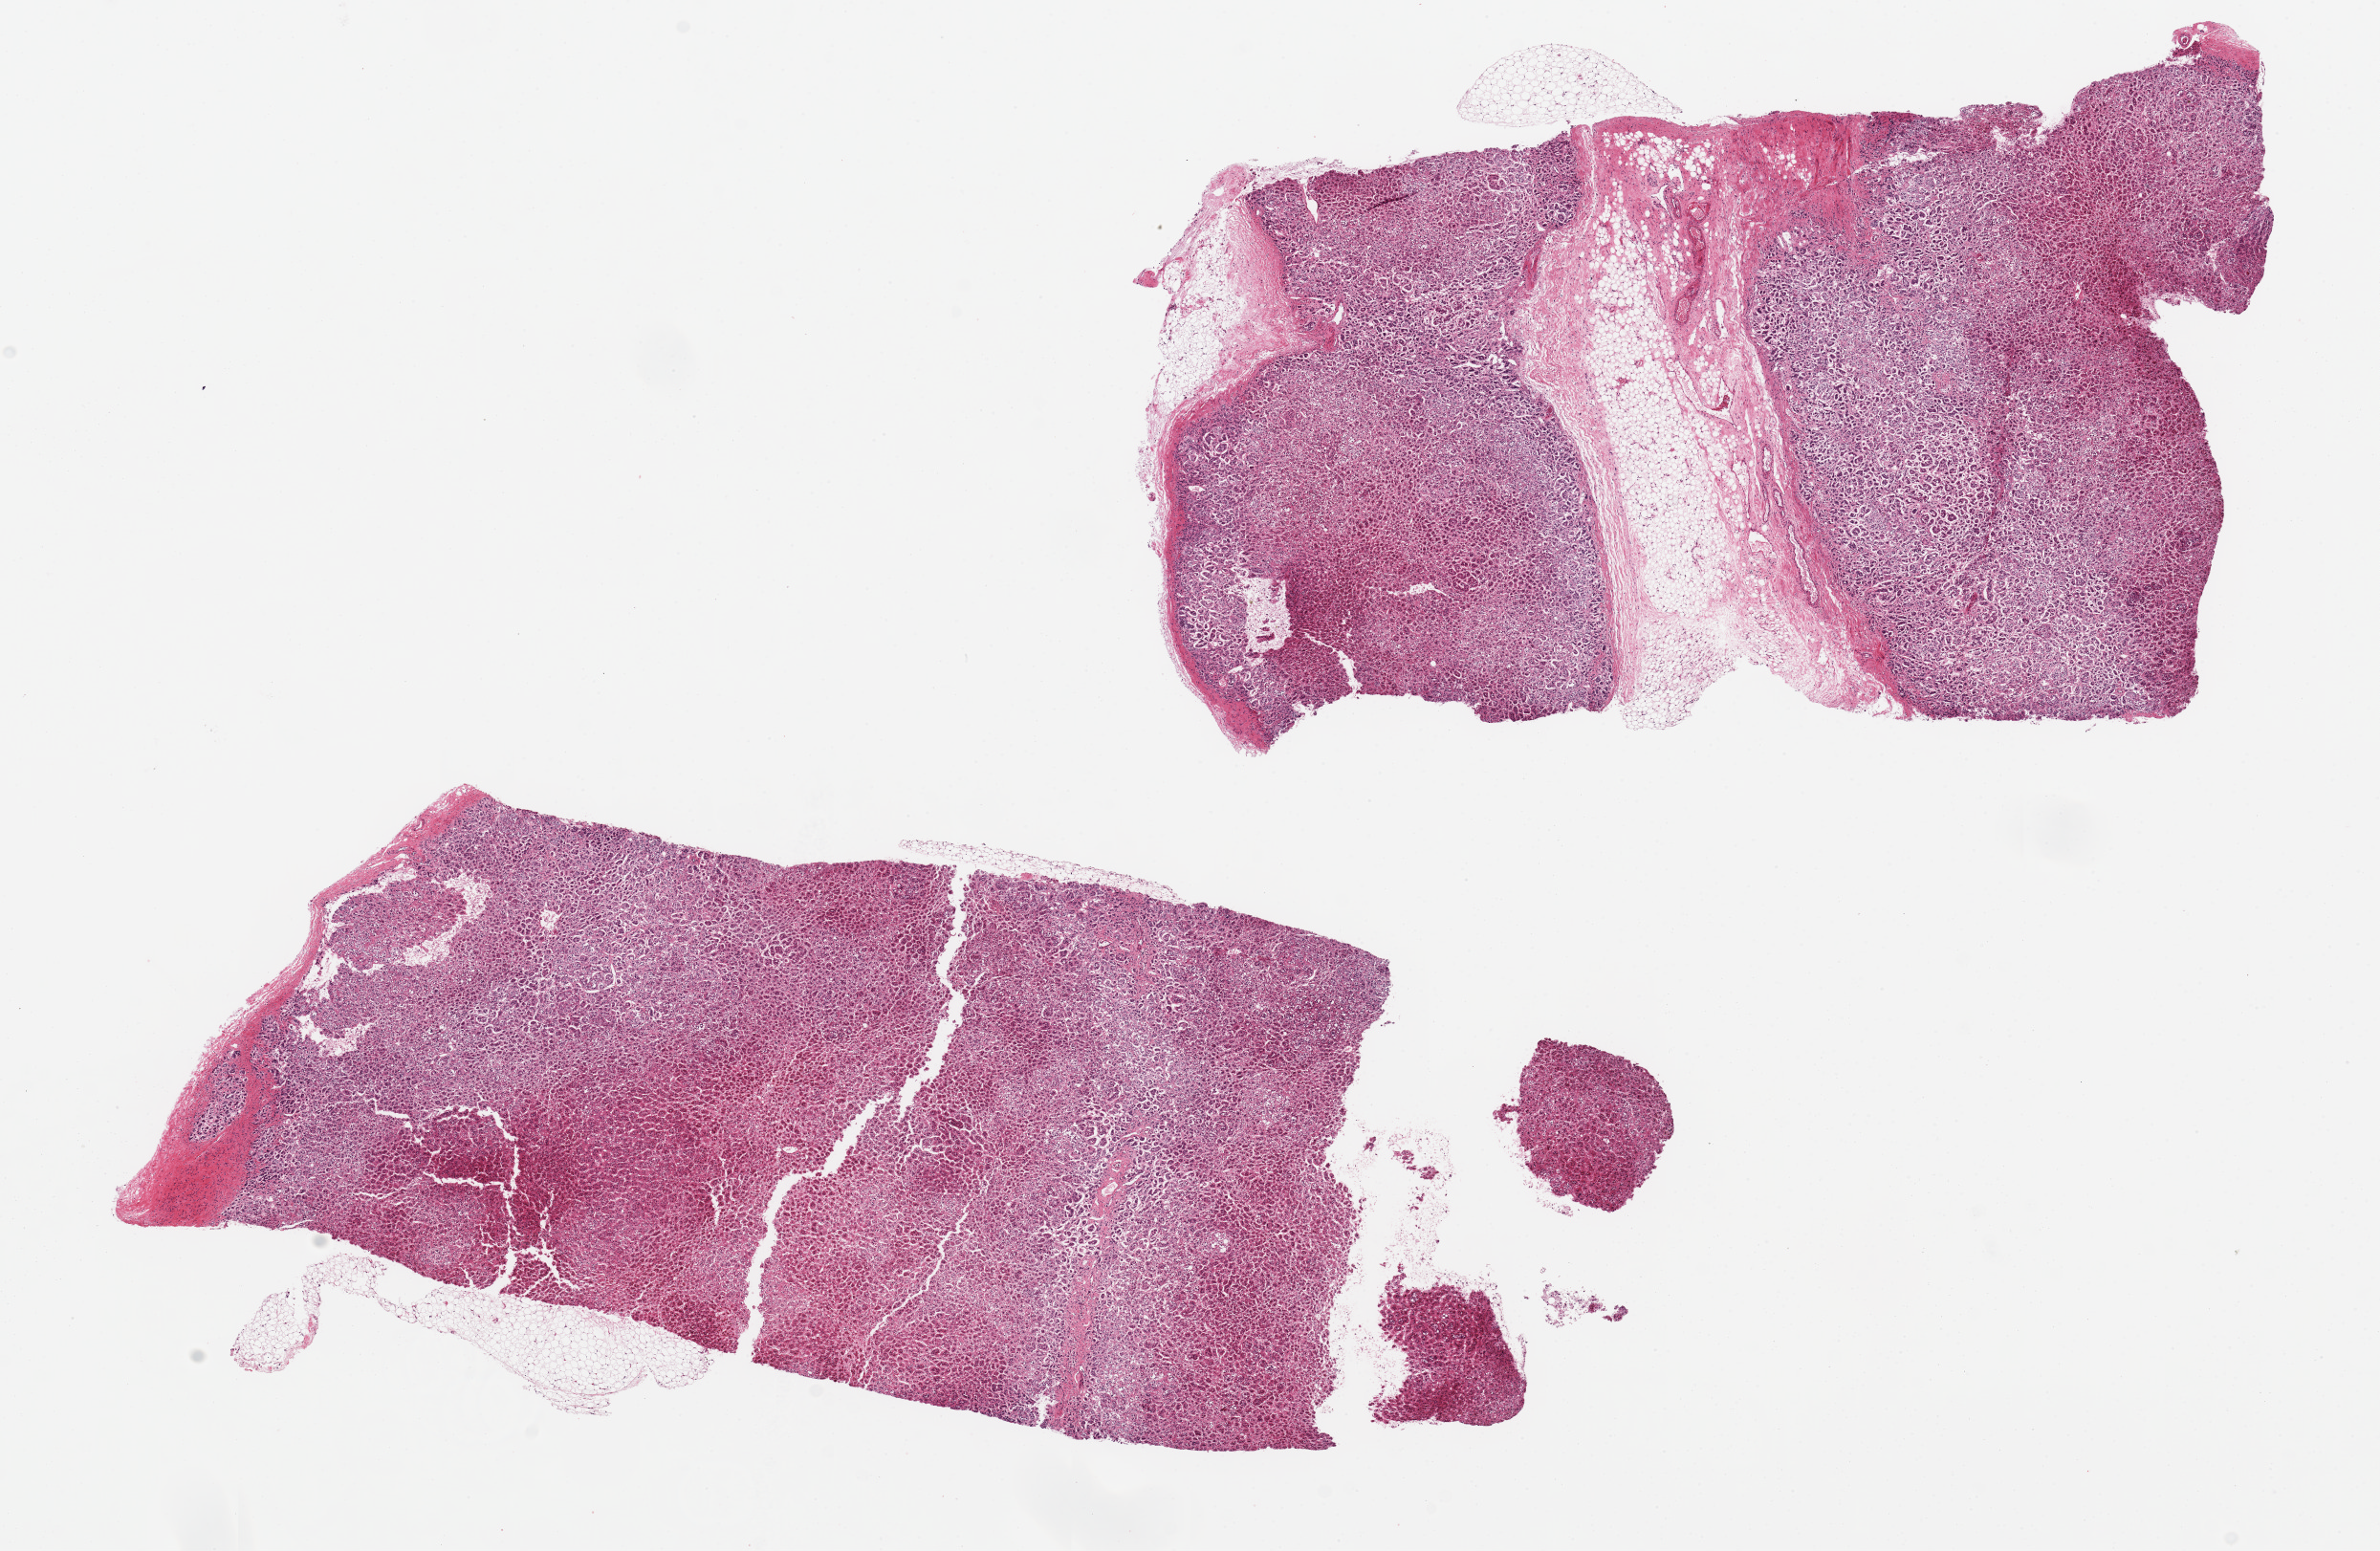
Digitized hematoxylin and eosin (H&E)-stained section — low-resolution overview of the scanned area, about 19.7 x 12.8 mm; PAXgene-fixed, paraffin-embedded tissue; section of adrenal gland (target tissue); tissue donor sample.
* pathologist's review note for this sample: 2 pieces 10x4&9x5 mm; 1 has 25% adipose